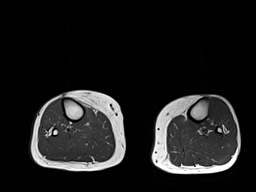
MRI of an extremity soft-tissue mass, one axial slice; position 18 of 32 along the scan axis; 6 mm slice thickness; 256 × 192 image matrix, field of view 375 × 281 mm. Female patient. Case-level facts recorded for this patient, not image findings: histological type: undifferentiated – high grade; grade: high; site of the primary tumour: right thigh.
Outlined on this slice (expert manual segmentation):
- gross tumour volume (mass): bounding box (x1, y1, x2, y2) in pixels: (83, 106, 97, 124)